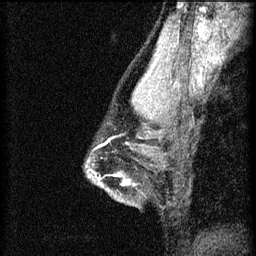
Breast MRI (dynamic contrast-enhanced), one sagittal slice; position 45 of 60 along the scan axis; 3 images stored at this slice position (order not interpretable as contrast timing); 1.5 T; TE 4.2 ms, TR 8.2 ms; 256 × 256 image matrix, field of view 180 × 180 mm. Patient: female, 44 years.
Annotated regions visible in this slice (semi-automatic segmentation, software-assisted and operator-edited):
- analysis volume of interest (the breast-tissue region the enhancement analysis was run in; not a lesion): bounding box (x1, y1, x2, y2) in pixels: (94, 172, 137, 205)
- tumour enhancement mask (voxels above the 70 % enhancement threshold inside the analysis volume of interest): (114, 176, 127, 181)